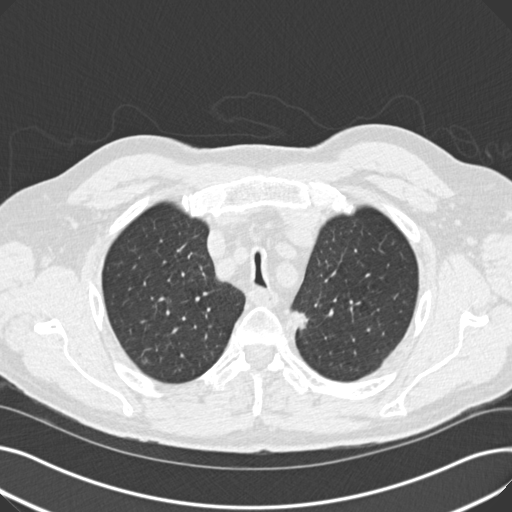
Axial slice from a low-dose chest CT screening exam, second annual screen, lung window (W 1500 / L -600 HU), 2 mm slice thickness, slice 42 of 187 in the series. Male participant, aged 70 years at enrolment. Current smoker at enrolment.
Expert-annotated lung lesion, bounding box (x1, y1, x2, y2) in pixels: (280, 299, 319, 341). The screening reader recorded 2 non-calcified nodules or masses ≥4 mm on this exam (left upper lobe, left lower lobe); which of them this box marks is not recorded. Lung cancer was diagnosed 581 days after this screen (after the third annual screen): mixed cell adenocarcinoma, left upper lobe, poorly differentiated (G3), stage IIB (AJCC 6th edition), 17 mm at pathology.